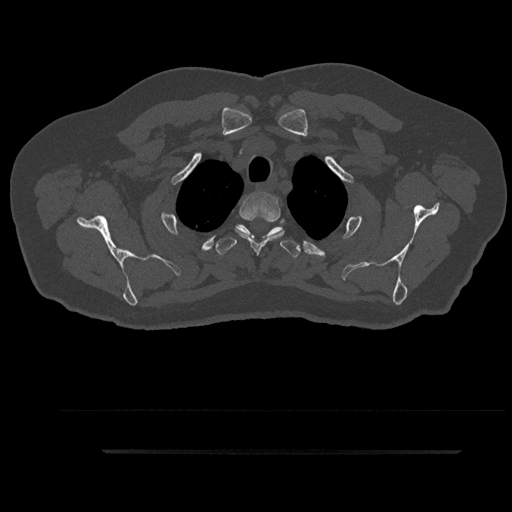
CT including the spine, one axial slice; position 743 of 797 along the scan axis; reconstruction kernel Br40s/3; bone window (W 1800 / L 400 HU); 512 × 512 image matrix, field of view 432 × 432 mm. Male patient, age 63 years. From the clinical record (not read from this slice): primary cancer: renal; vertebrae with lytic lesions (as recorded): T8.
Annotated regions visible in this slice (semi-automatically segmented with operator editing):
- T2 vertebra: bounding box <235,191,284,254> (left, top, right, bottom; pixels)
- T3 vertebra: <214,224,301,258>